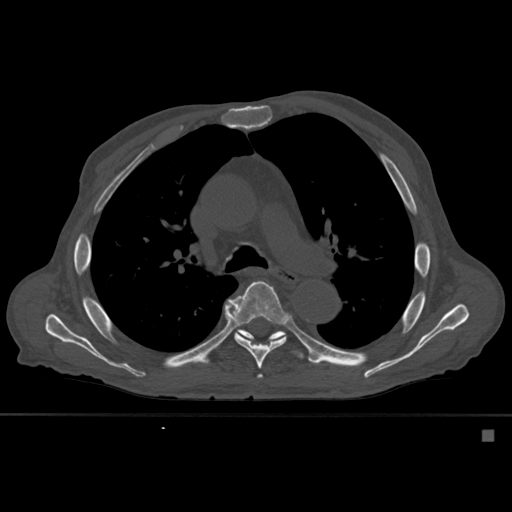
CT including the spine, one axial slice. Position 381 of 527 along the scan axis. Bone window (W 1800 / L 400 HU). 1.5 mm slice thickness. 512 × 512 image matrix, field of view 373 × 373 mm. Patient: male, 78 years. From the clinical record (not read from this slice): primary cancer: prostate.
Annotated regions visible in this slice (semi-automatic segmentation, software-assisted and operator-edited):
- T5 vertebra: bounding box (x1, y1, x2, y2) in pixels: (257, 374, 263, 379)
- T6 vertebra: (225, 281, 290, 369)
- T7 vertebra: (218, 329, 305, 359)